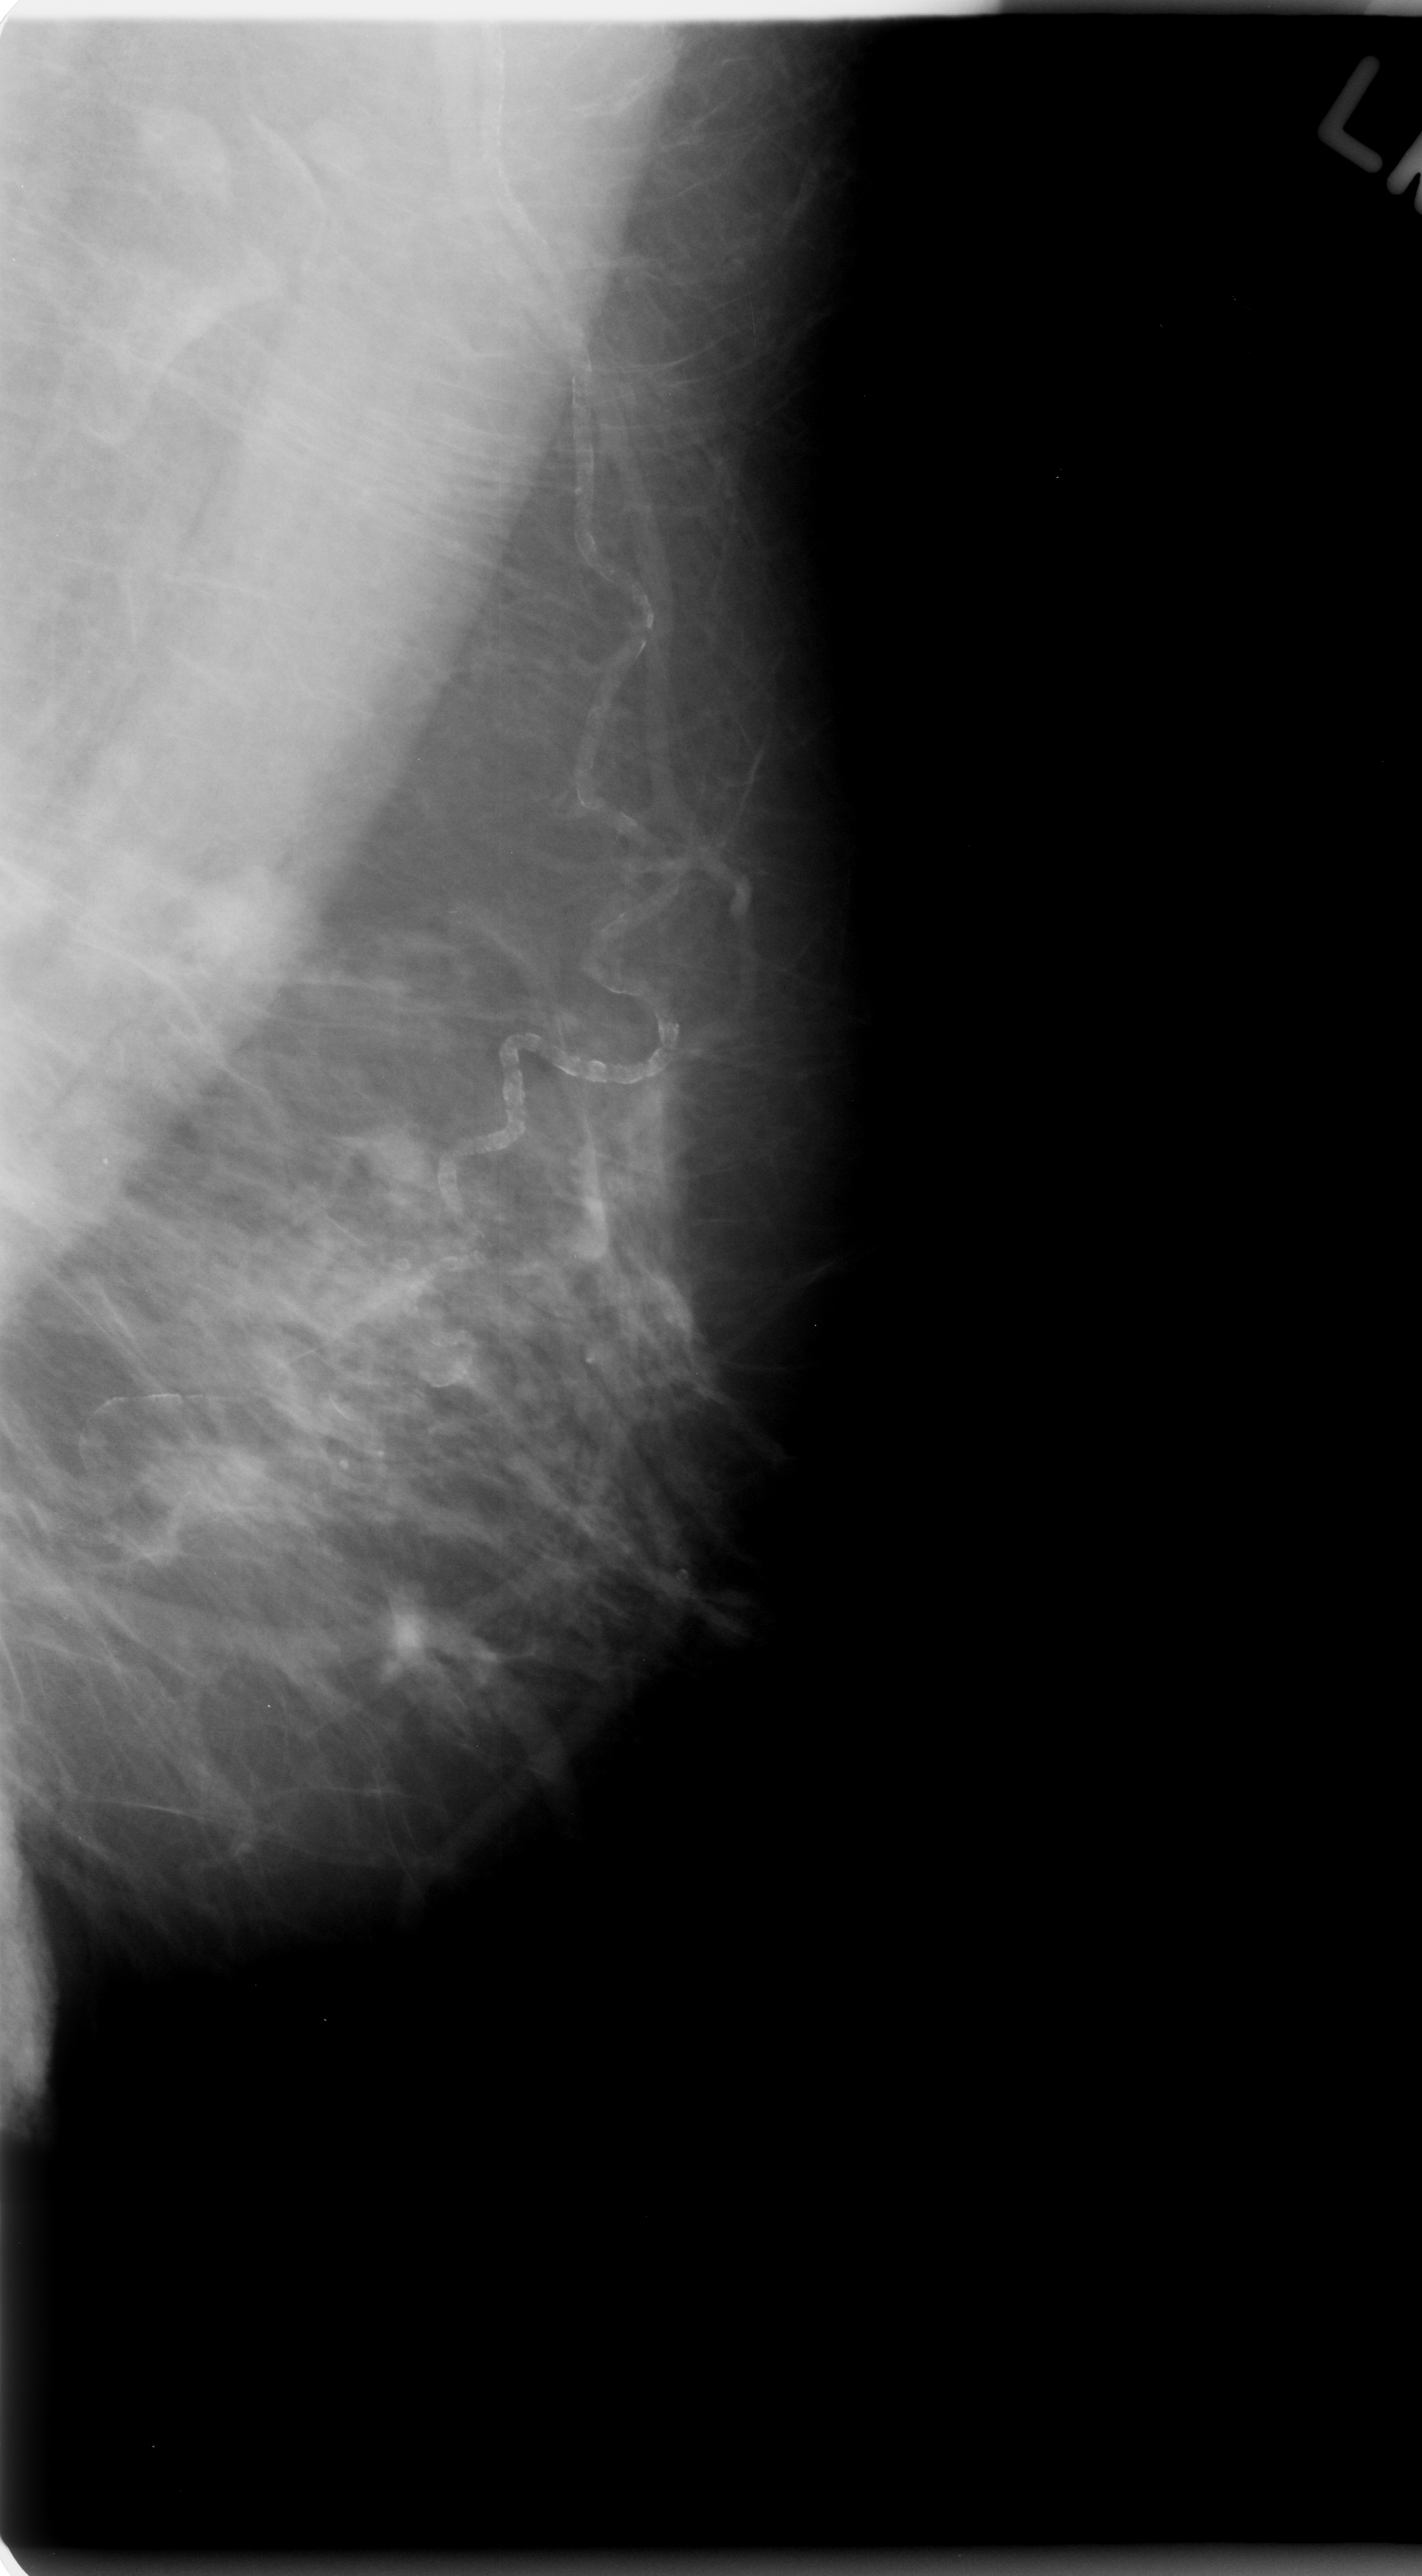
Mammogram (digitized film), left breast, mediolateral oblique (MLO) view, BI-RADS breast density category 2 (scale 1–4).
- Marked findings (only marked abnormalities are described; nothing is implied about the rest of the image): mass, shape lobulated, margins microlobulated; BI-RADS assessment category 4; subtlety rating 4 on a 1 (subtle) to 5 (obvious) scale; pathology result (as recorded, not read from the image): malignant.